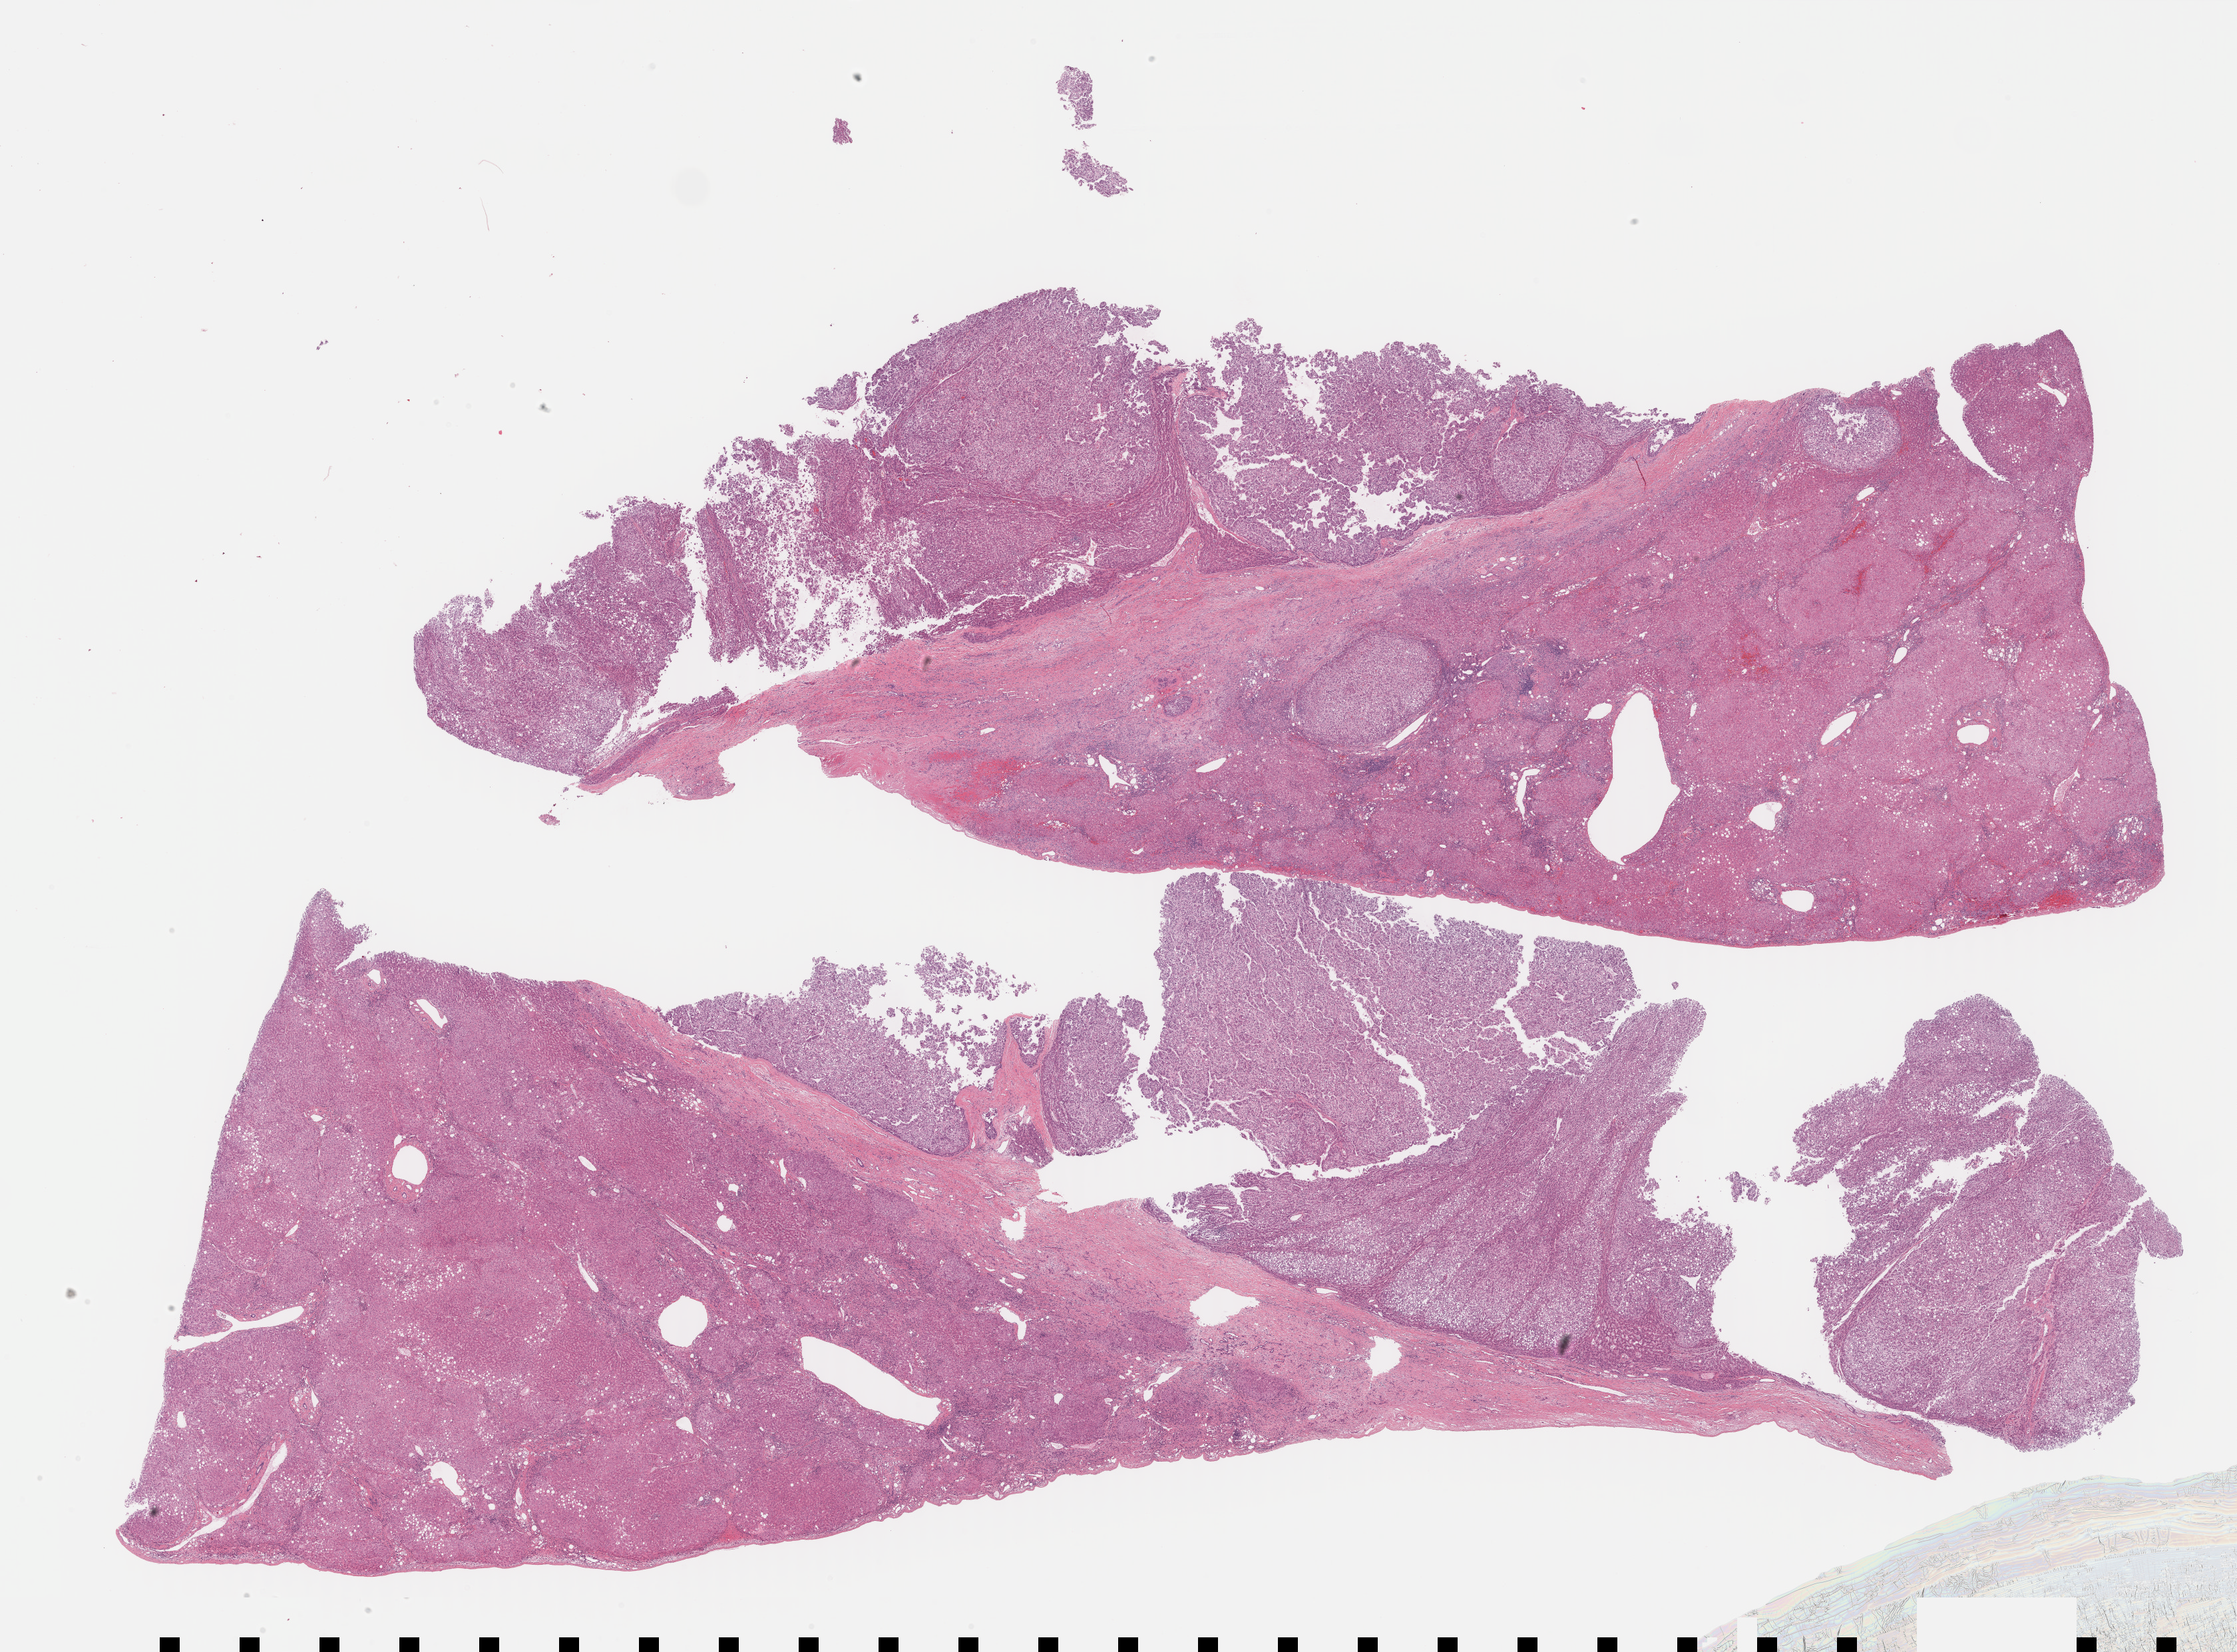
Digitized H&E tissue section (whole slide), shown as a low-resolution overview of the whole scanned area (about 27.2 x 20.1 mm, acquisition: 40x scan); FFPE section; primary tumour sample from the liver. Patient: male, age at initial diagnosis 71 years.
Diagnosis: Hepatocellular carcinoma, NOS.